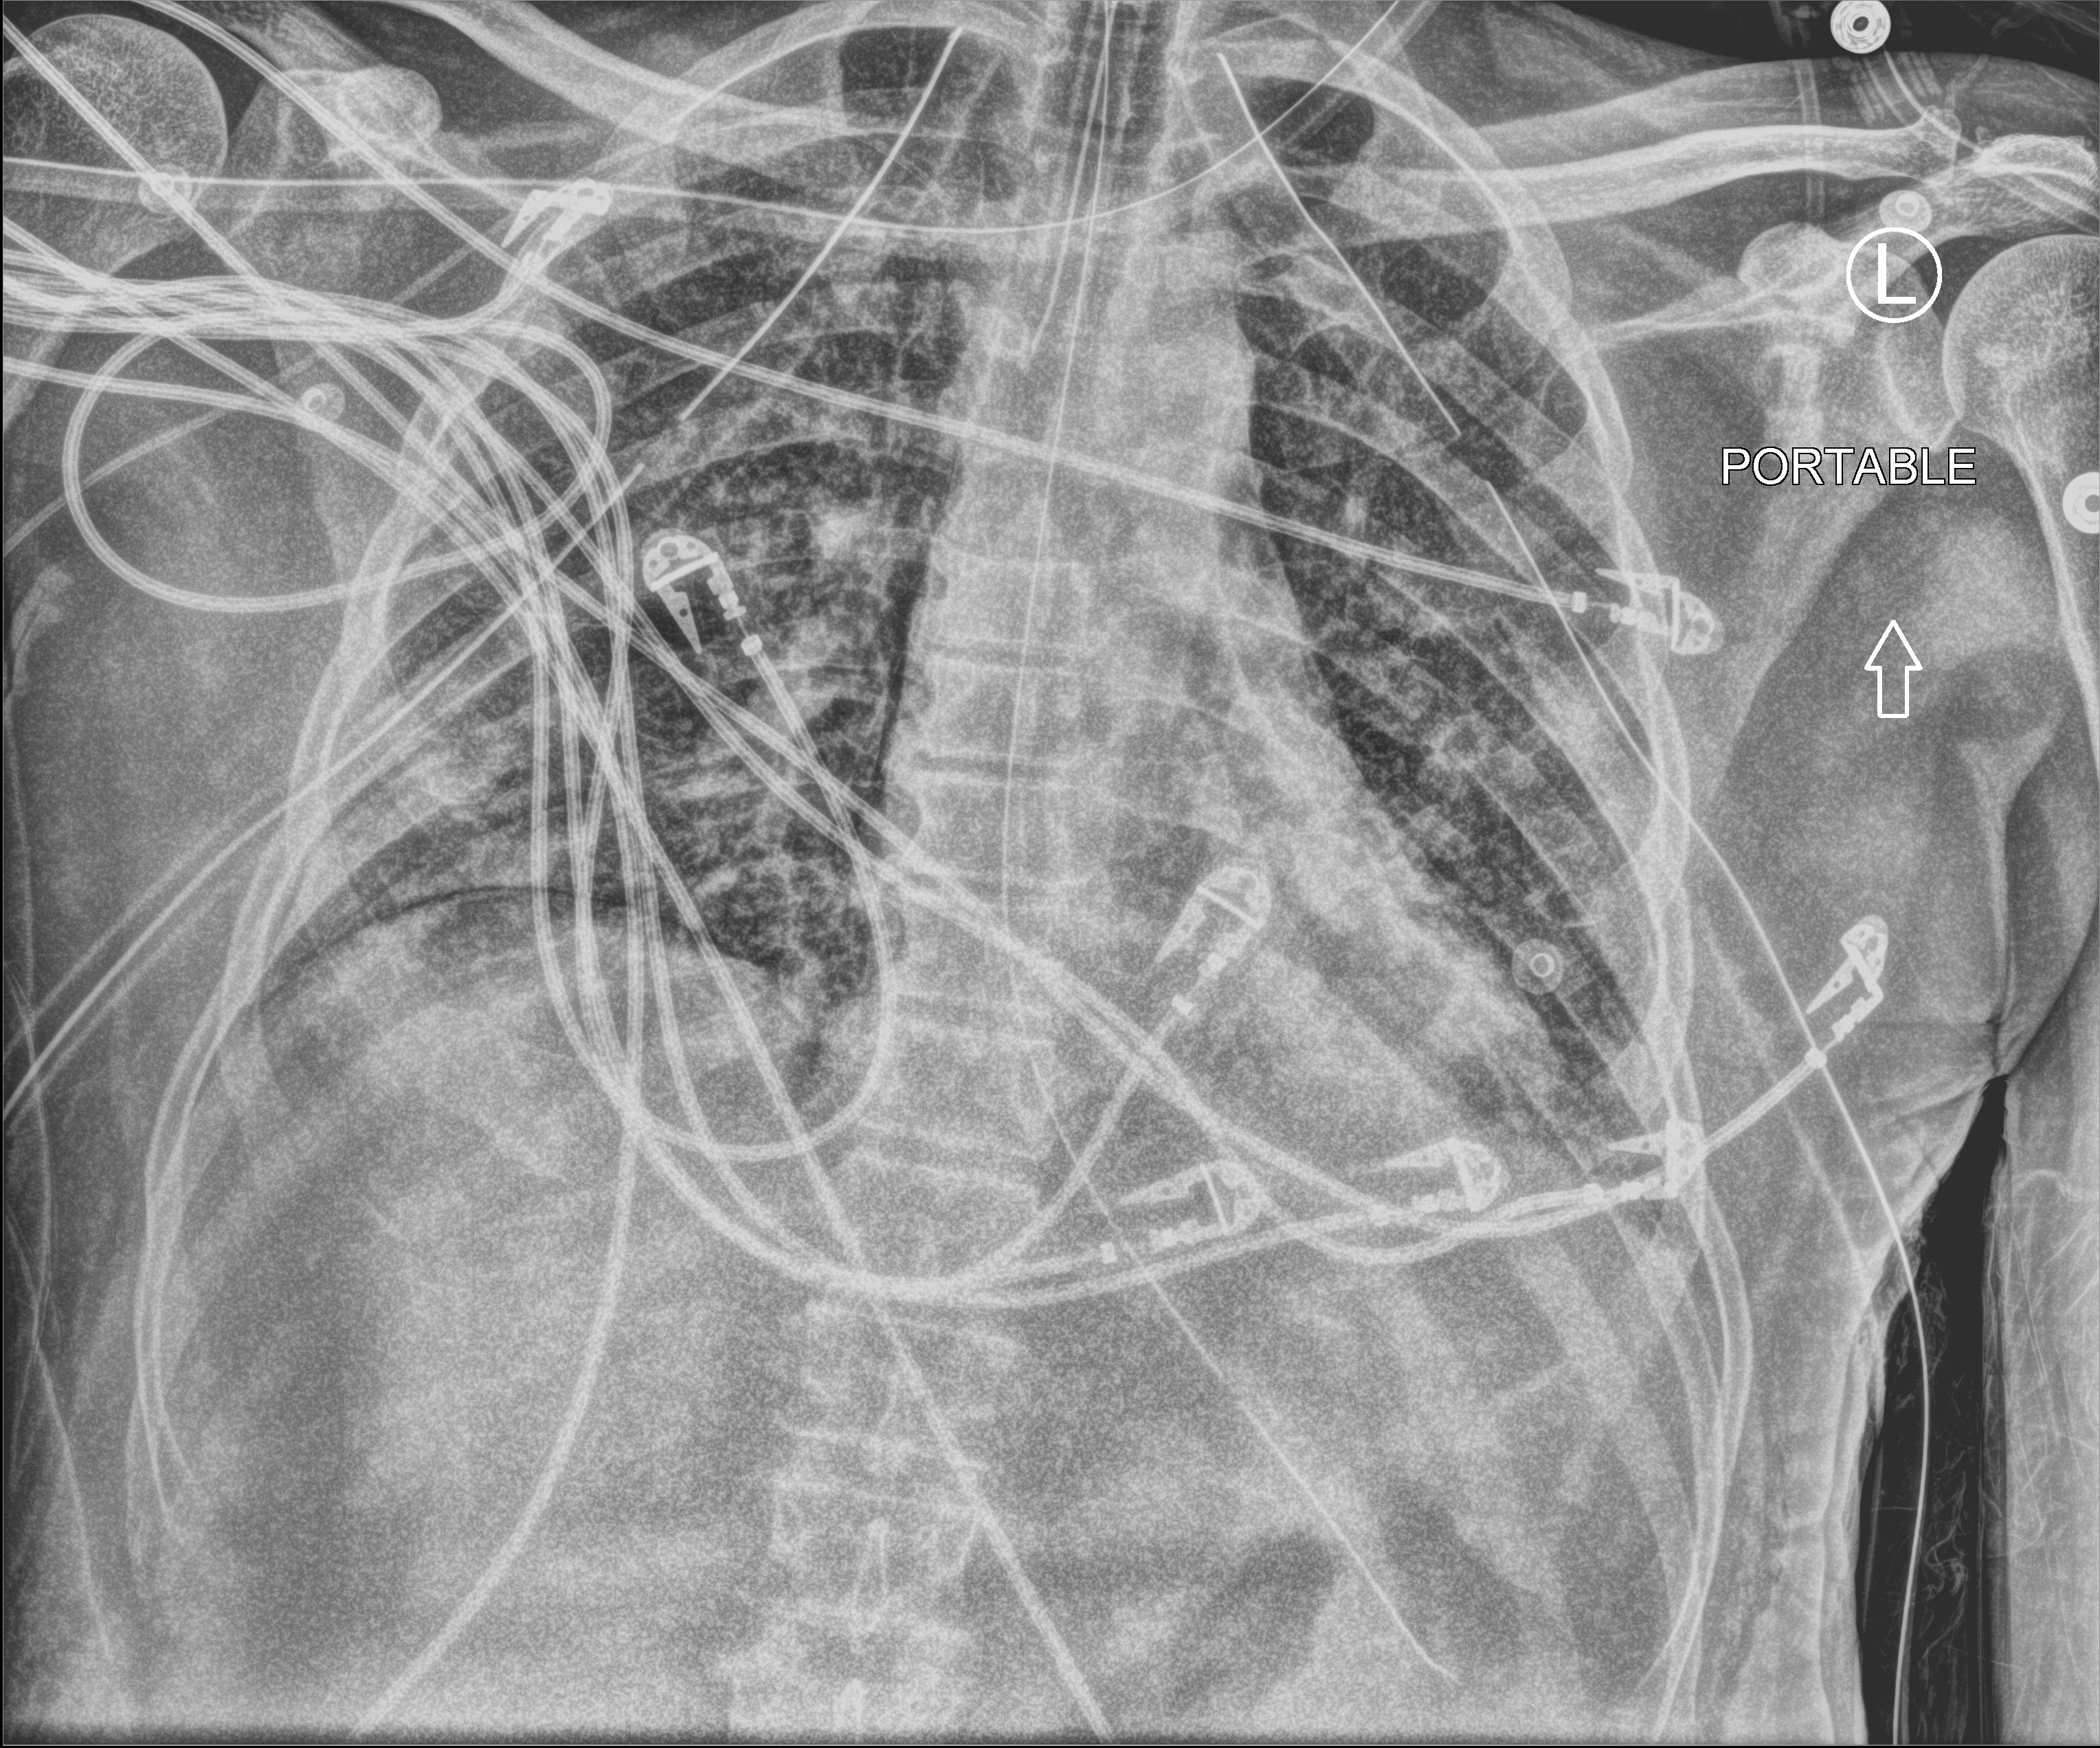
Bedside chest radiograph (computed radiography); anteroposterior (AP) projection. Male patient hospitalised with COVID-19, age 18–59 years.
Admission-level facts for this patient (not findings on this image; timing relative to this image not recorded): mechanically ventilated during this hospital stay: yes.